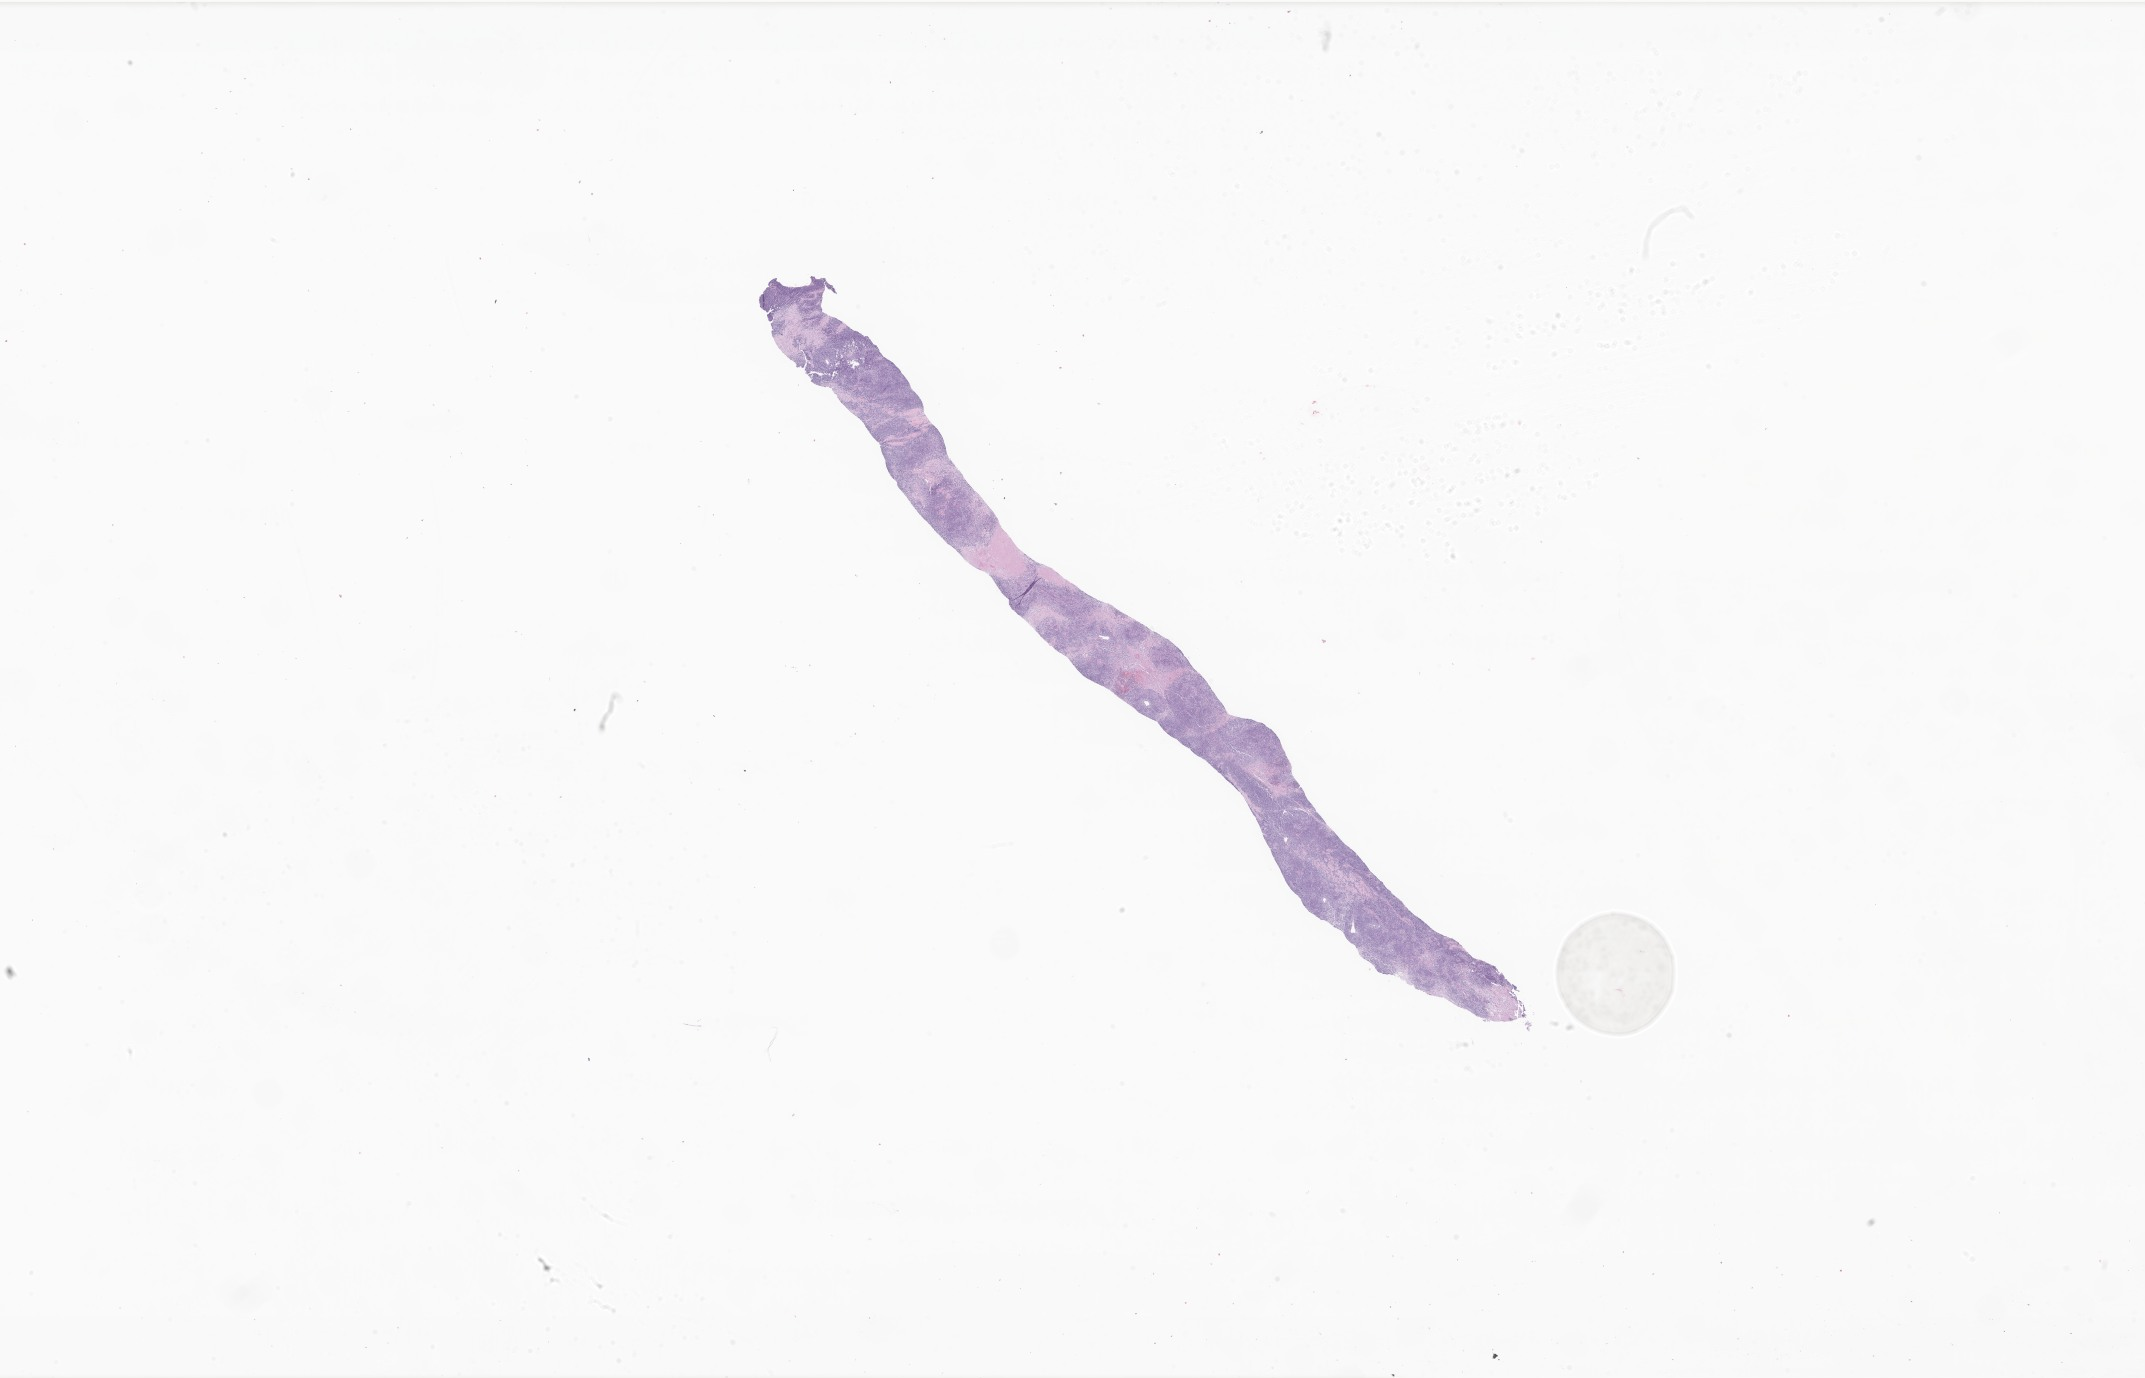
Digitized H&E-stained section of tumor tissue from the upper limb — shown as a low-resolution overview of the whole scanned area (about 36.2 x 23.2 mm), formalin-fixed paraffin-embedded section. Patient female; age 158 months (13 years 2 months).
- recorded diagnosis: Rhabdomyosarcoma, NOS